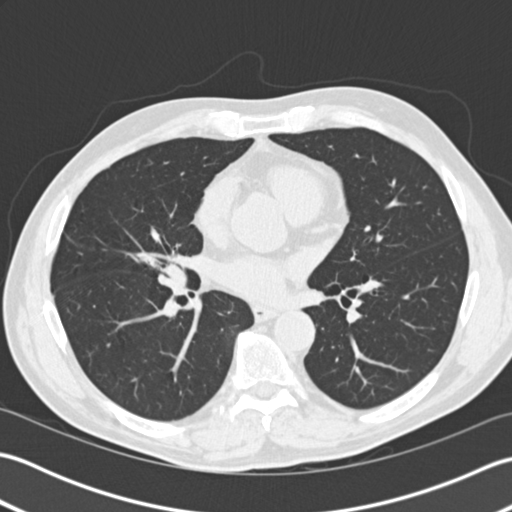
Low-dose screening chest CT, axial slice, second annual screen, lung window (W 1500 / L -600 HU), 2 mm slice thickness, 512 × 512 image matrix, field of view 350 × 350 mm. Male participant, aged 57 years at enrolment.
Expert-annotated lung lesion, bounding box <154,250,196,293> (left, top, right, bottom; pixels). Screening reader's record for this exam: no non-calcified nodule ≥4 mm recorded. Official screen result: negative screen, significant abnormalities not suspicious for lung cancer. Lung cancer was diagnosed 483 days after this screen: carcinoid tumor, NOS, right middle lobe, carcinoid, stage not assessed, 15 mm at pathology.